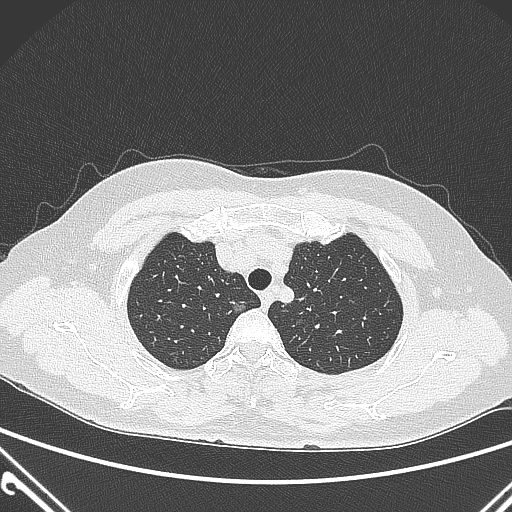
Chest CT, one axial slice; slice 235 of 300 in the series (ordered by position); lung window (W 1500 / L -600 HU); 512 × 512 image matrix, field of view 350 × 350 mm. Patient: female, 54 years. From the clinical record (not read from this slice): clinical TNM (as recorded): T1a N0 M0; histopathological grade: G1.
Structures marked on this image (bounding box drawn by a radiologist):
- lung tumour (recorded histology: adenocarcinoma): box from (x=226, y=297) to (x=259, y=333) px